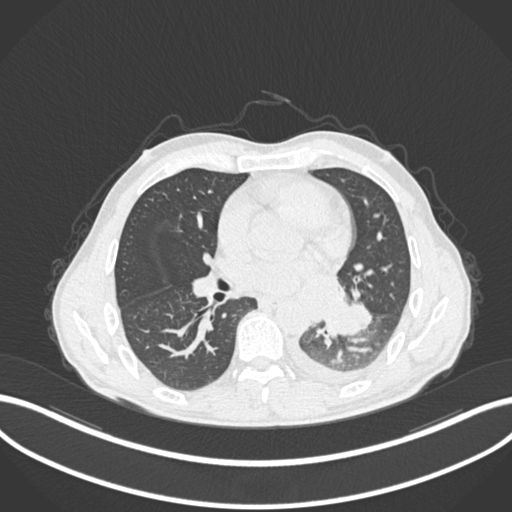
Chest CT, one axial slice; slice 117 of 222 in the series (ordered by position); 120 kVp; lung window (W 1500 / L -600 HU); 1 mm slice thickness; 512 × 512 image matrix. Patient: male, 47 years. From the clinical record (not read from this slice): clinical TNM (as recorded): T3 N1 M1c.
Structures marked on this image (rectangle marked by the reading radiologist):
- lung tumour (recorded histology: small cell carcinoma): bounding box <325,296,364,340> (left, top, right, bottom; pixels)